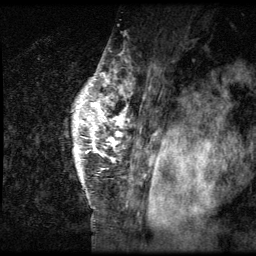
Breast MRI (dynamic contrast-enhanced), one sagittal slice. Slice 52 of 64 in the series (ordered by position). 3 images stored at this slice position (order not interpretable as contrast timing). 1.5 T. TE 4.2 ms, TR 9 ms. 2.5 mm slice thickness. 256 × 256 image matrix. Patient: female, 50 years. Case-level facts recorded for this patient, not image findings: setting: breast cancer imaged before/during neoadjuvant chemotherapy; receptor status: triple-negative.
Annotated regions visible in this slice (semi-automatic segmentation, software-assisted and operator-edited):
- analysis volume of interest (the breast-tissue region the enhancement analysis was run in; not a lesion): bounding box <24,39,137,212> (left, top, right, bottom; pixels)
- tumour enhancement mask (voxels above the 140 % enhancement threshold inside the analysis volume of interest): <73,70,137,202>